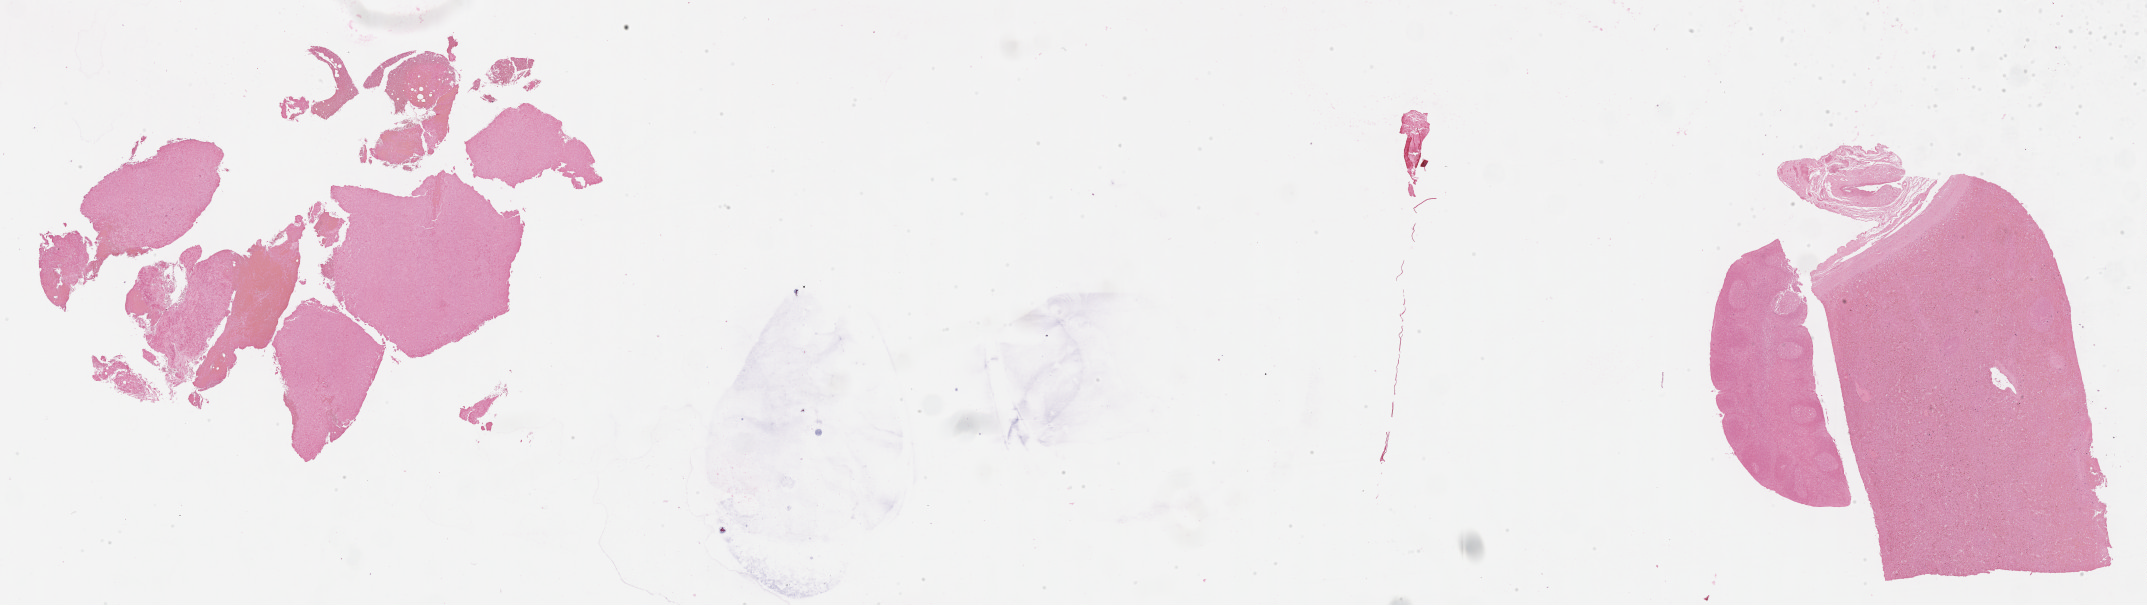
In-situ hybridisation whole-slide image, Epstein–Barr virus-encoded RNA (EBER) probe, low-resolution overview of the scanned area, about 34.7 x 9.8 mm, tumor tissue, anatomic site: lymph node. Patient female; 71 years old.
* histologic diagnosis: Diffuse large B-cell lymphoma, NOS